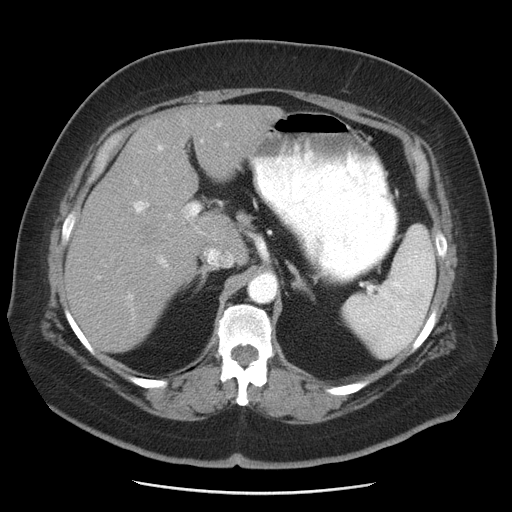
Contrast-enhanced abdominal CT, one axial slice. Position 31 of 55 along the scan axis. Reconstruction kernel STANDARD. Soft-tissue window (W 400 / L 40 HU). 5 mm slice thickness. 512 × 512 image matrix, field of view 380 × 380 mm. Female patient, age 52 years. From the clinical record (not read from this slice): diagnosis: colorectal cancer liver metastases, imaged before liver resection; multiple liver metastases: yes; largest metastasis: 2.5 cm; disease in both lobes: yes.
Structures marked on this image (expert manual segmentation):
- liver: bounding box (x1, y1, x2, y2) in pixels: (65, 105, 284, 353)
- planned liver remnant (the part of the liver to remain after resection): (65, 186, 207, 353)
- portal vein (with intrahepatic branches): (117, 139, 204, 298)